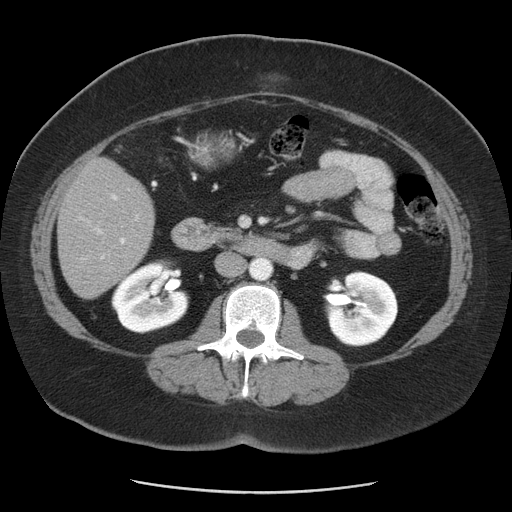
Contrast-enhanced abdominal CT, one axial slice; position 16 of 55 along the scan axis; 120 kVp; intravenous contrast given; soft-tissue window (W 400 / L 40 HU); 512 × 512 image matrix. Female patient, age 52 years. From the clinical record (not read from this slice): diagnosis: colorectal cancer liver metastases, imaged before liver resection; multiple liver metastases: yes; largest metastasis: 2.5 cm; disease in both lobes: yes.
Outlined on this slice (expert manual segmentation):
- liver: bounding box [x1, y1, x2, y2] px = [59, 157, 155, 299]
- planned liver remnant (the part of the liver to remain after resection): [59, 189, 143, 299]
- portal vein (with intrahepatic branches): [77, 192, 140, 260]